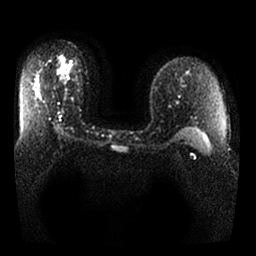
Breast MRI, one axial slice. Position 17 of 25 along the scan axis. Diffusion-weighted series; image 2 of 4 stored at this slice position (different b-values; order by instance number). 1.5 T. 4 mm slice thickness. 256 × 256 image matrix. Female patient.
Annotated regions visible in this slice (manually delineated by an expert):
- tumour on diffusion-weighted imaging: bounding box [x1, y1, x2, y2] px = [58, 69, 68, 81]